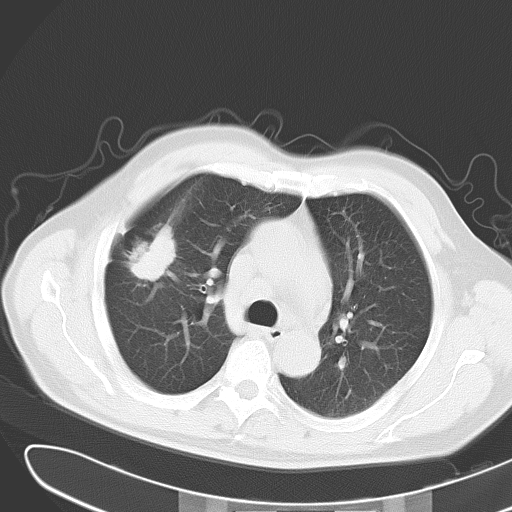
Chest CT, one axial slice. Position 21 of 31 along the scan axis. Lung window (W 1500 / L -600 HU). 512 × 512 image matrix, field of view 364 × 364 mm. Patient: male, 59 years. From the clinical record (not read from this slice): clinical TNM (as recorded): T2 N3 M0.
Outlined on this slice (rectangle marked by the reading radiologist):
- lung tumour (recorded histology: adenocarcinoma): box from (x=134, y=224) to (x=180, y=285) px